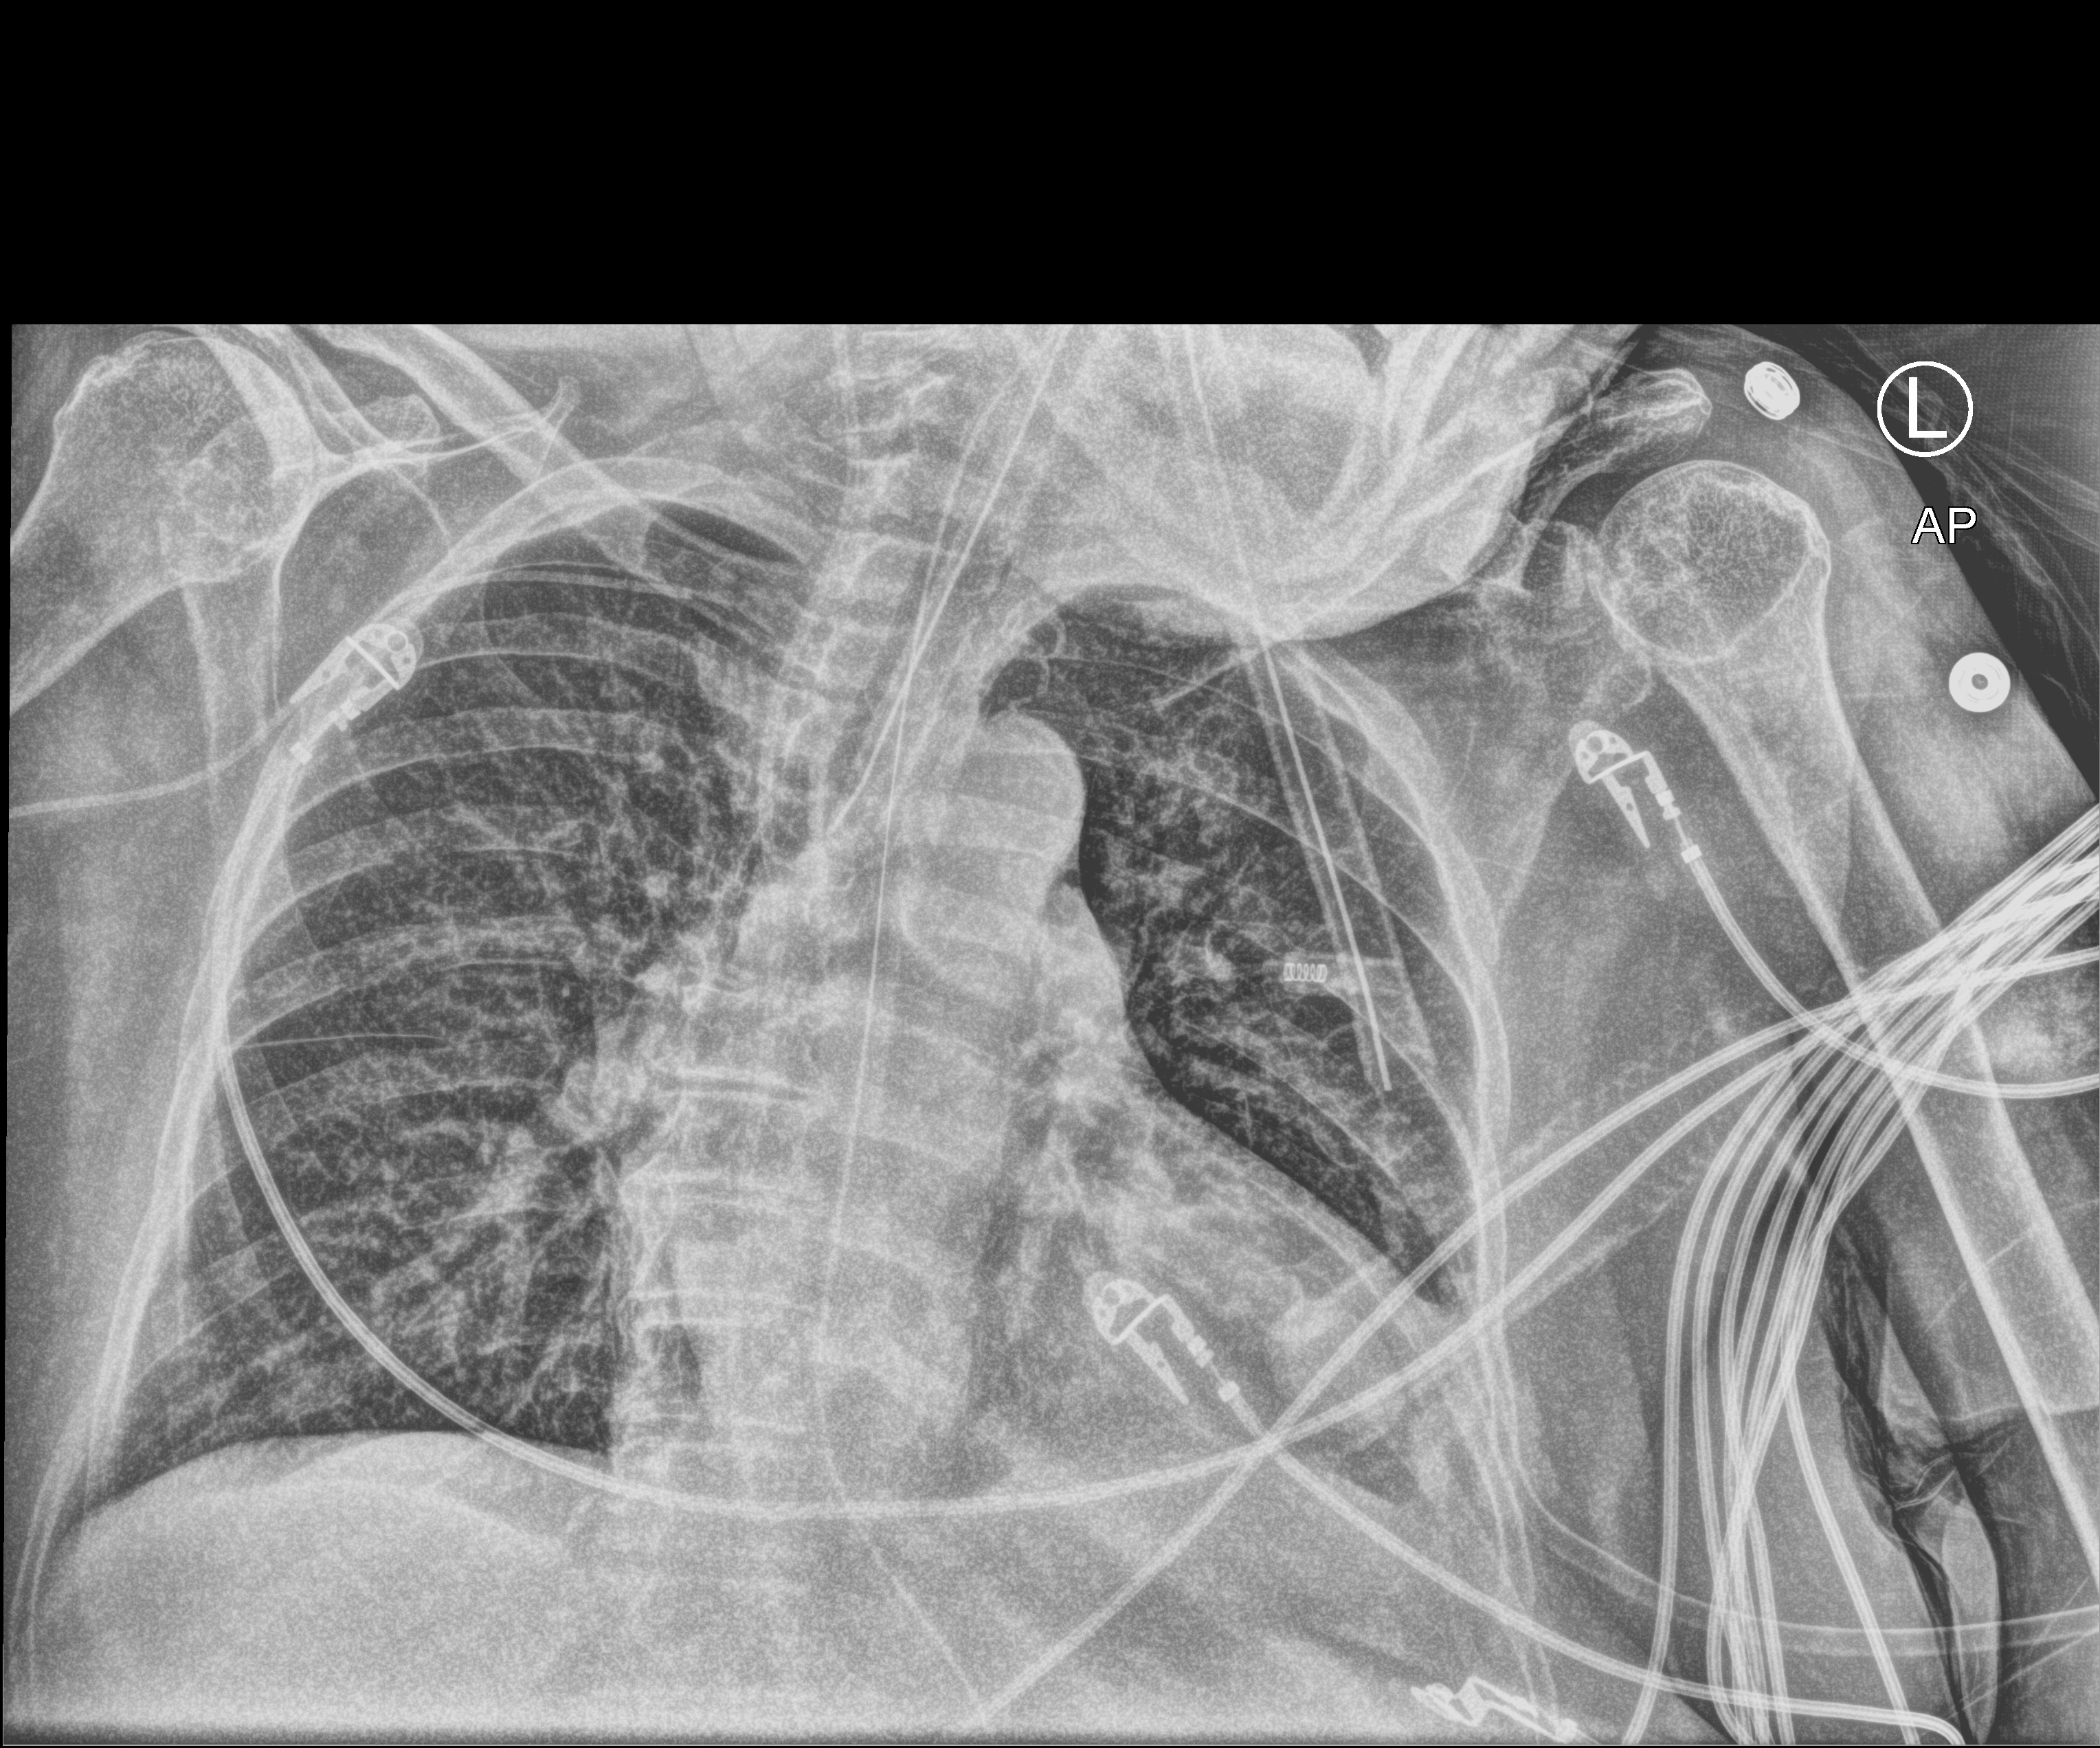
Chest X-ray (portable), anteroposterior (AP) projection. Female patient hospitalised with COVID-19, age 75–90 years.
From the hospital-stay record, not from the radiograph (when in the stay this image was taken is not recorded): length of hospital stay: 29 days; mechanically ventilated during this hospital stay: yes.